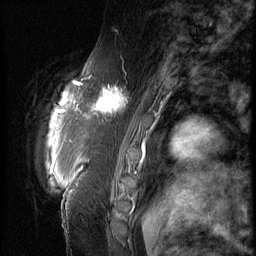
Breast MRI (dynamic contrast-enhanced), one sagittal slice; slice 17 of 66 in the series (ordered by position); 3 images stored at this slice position (order not interpretable as contrast timing); 1.5 T; TE 4.2 ms, TR 9 ms; 2.5 mm slice thickness; 256 × 256 image matrix. Female patient, age 57 years. From the clinical record (not read from this slice): setting: breast cancer imaged before/during neoadjuvant chemotherapy; receptor status: triple-negative.
Structures marked on this image (semi-automatic segmentation, software-assisted and operator-edited):
- analysis volume of interest (the breast-tissue region the enhancement analysis was run in; not a lesion): bounding box (x1, y1, x2, y2) in pixels: (86, 74, 138, 129)
- tumour enhancement mask (voxels above the 140 % enhancement threshold inside the analysis volume of interest): (92, 86, 125, 115)